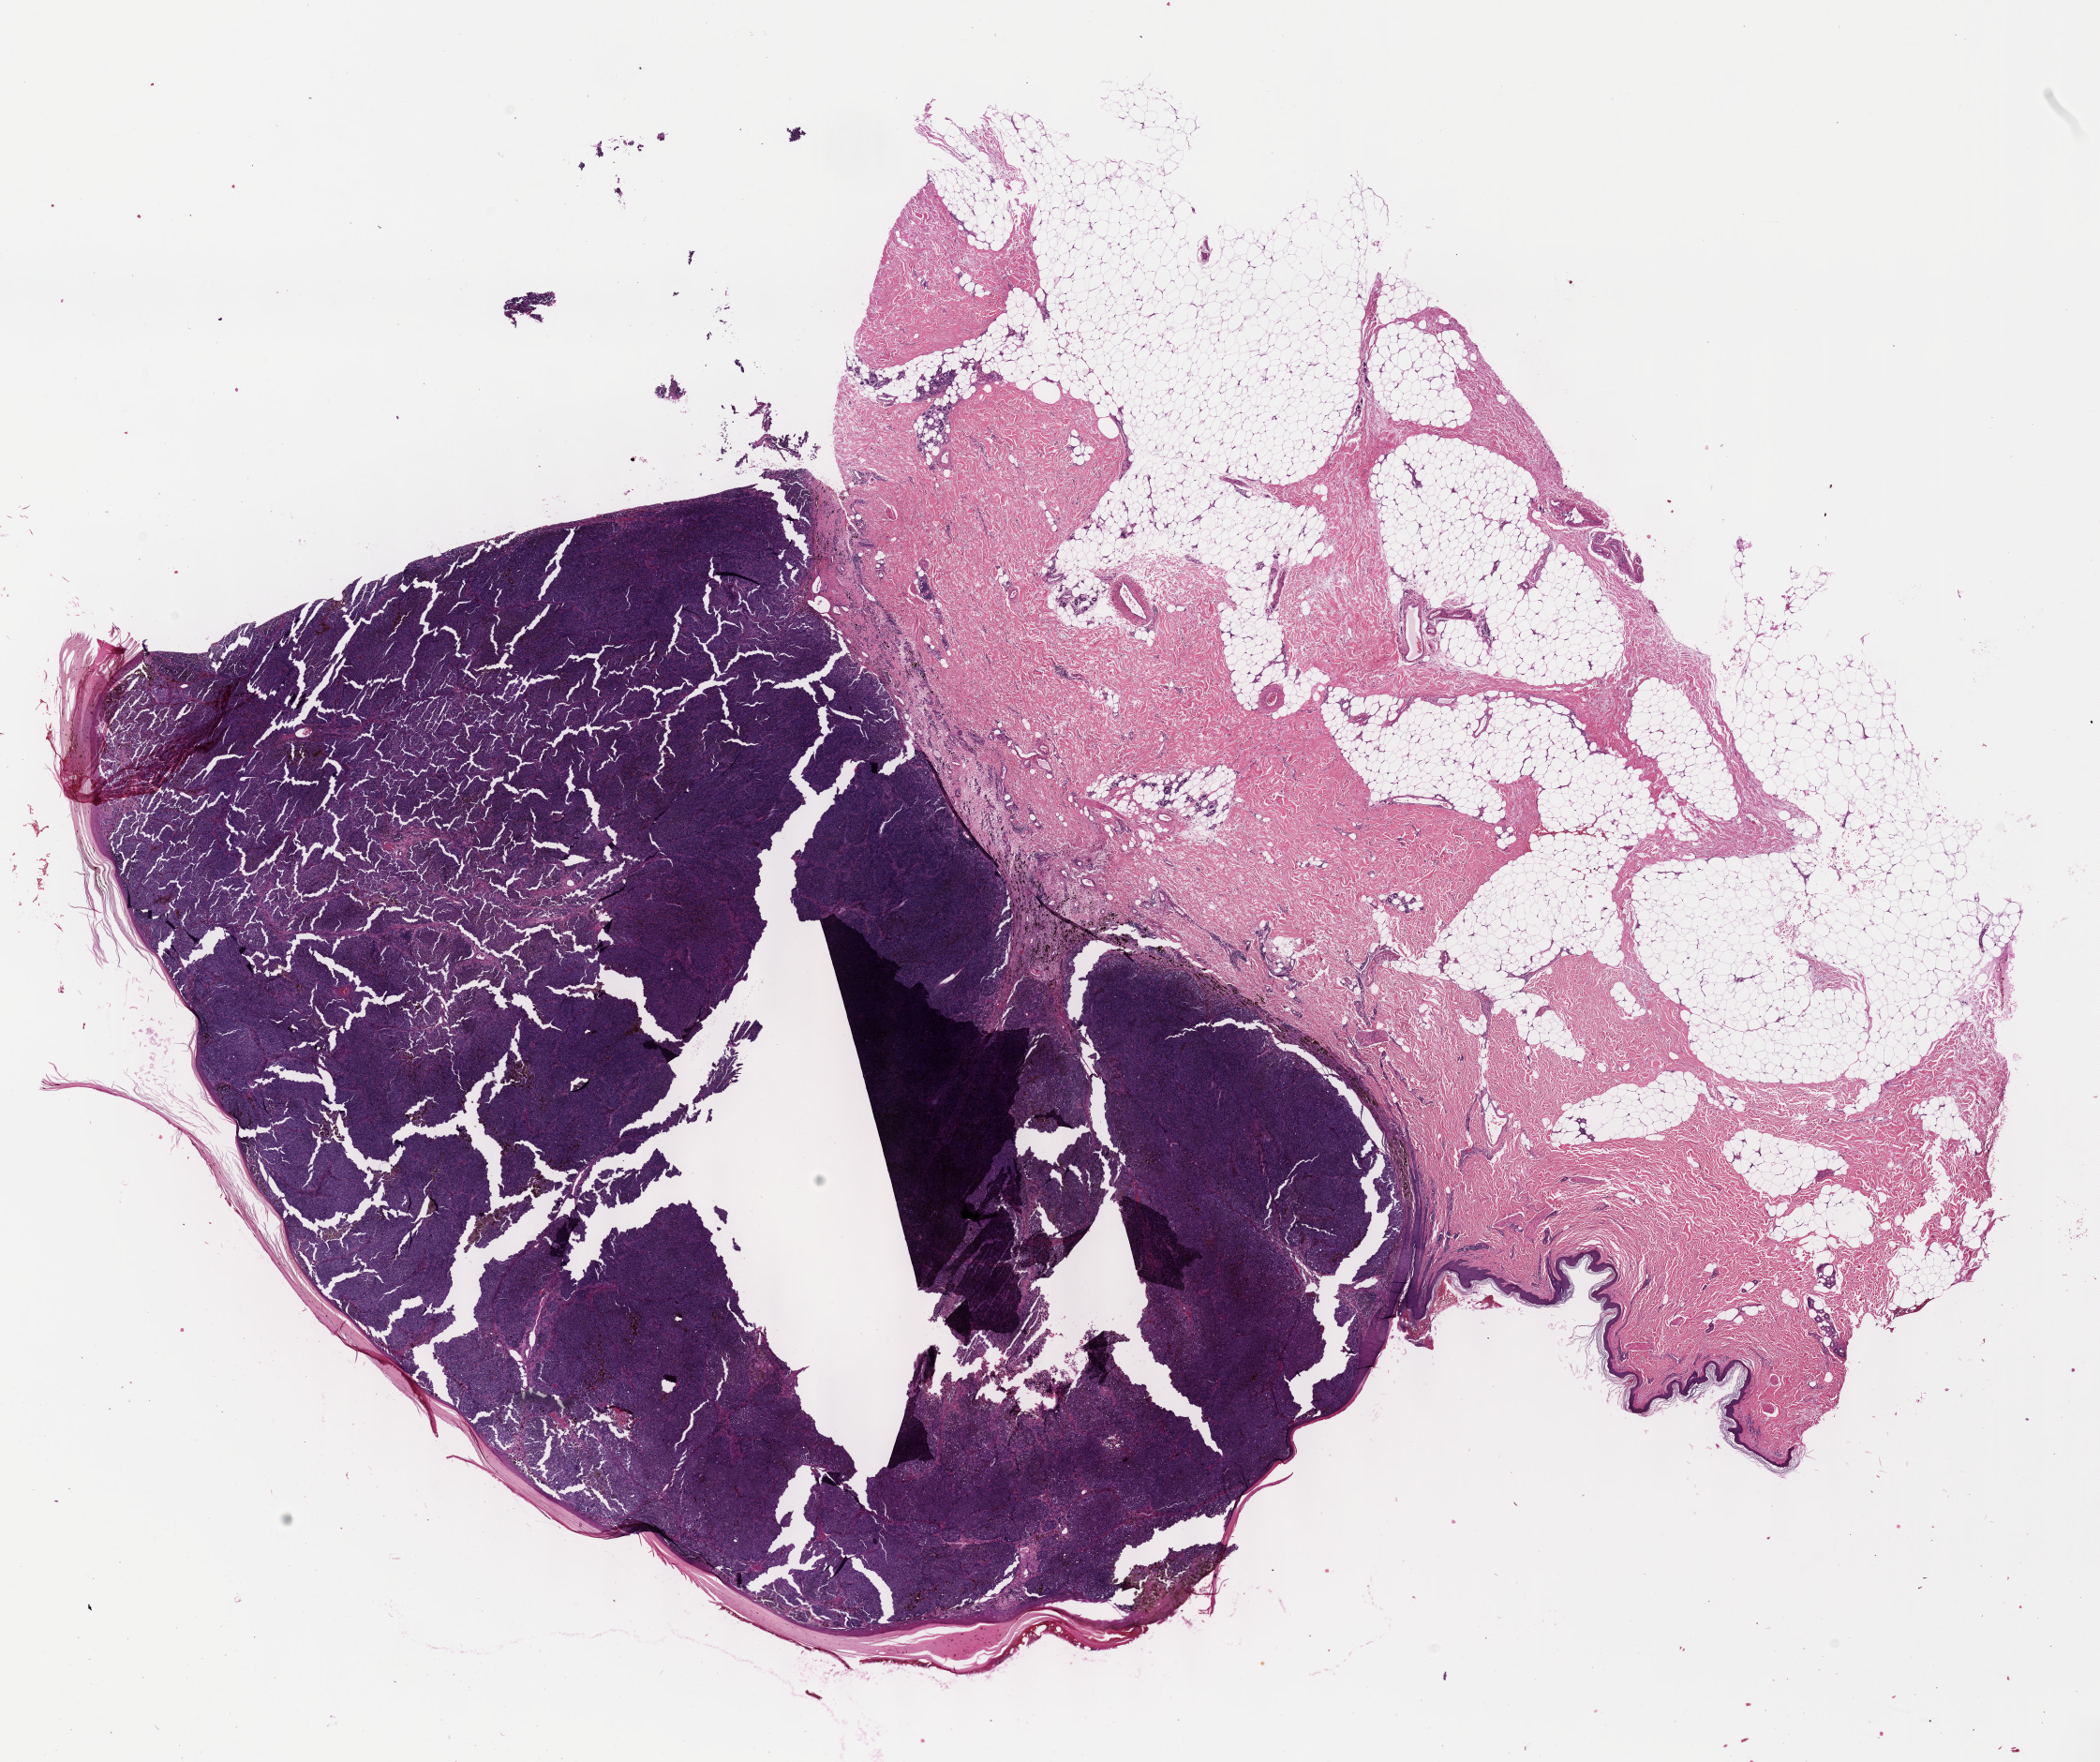
H&E whole-slide image, a low-resolution overview of the entire scanned area, about 18.1 x 15.2 mm (from a 40x scan); formalin-fixed paraffin-embedded (FFPE) diagnostic section; primary tumour sample from the skin. Male patient; age at initial diagnosis 77 years.
* AJCC pathologic stage: IIC (7th edition)
* TNM: T4b N0 M0
* pathologic diagnosis: Mixed epithelioid and spindle cell melanoma